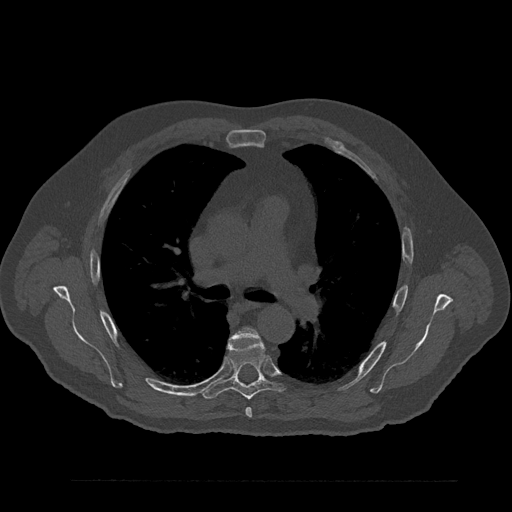
CT including the spine, one axial slice. Position 565 of 797 along the scan axis. Reconstruction kernel Br40s/3. 120 kVp. Bone window (W 1800 / L 400 HU). 0.5 mm slice thickness. 512 × 512 image matrix, field of view 430 × 430 mm. Patient: male, 61 years. Case-level facts recorded for this patient, not image findings: primary cancer: prostate.
Outlined on this slice (semi-automatically segmented with operator editing):
- T5 vertebra: bounding box [x1, y1, x2, y2] px = [232, 328, 259, 418]
- T6 vertebra: [202, 340, 286, 400]